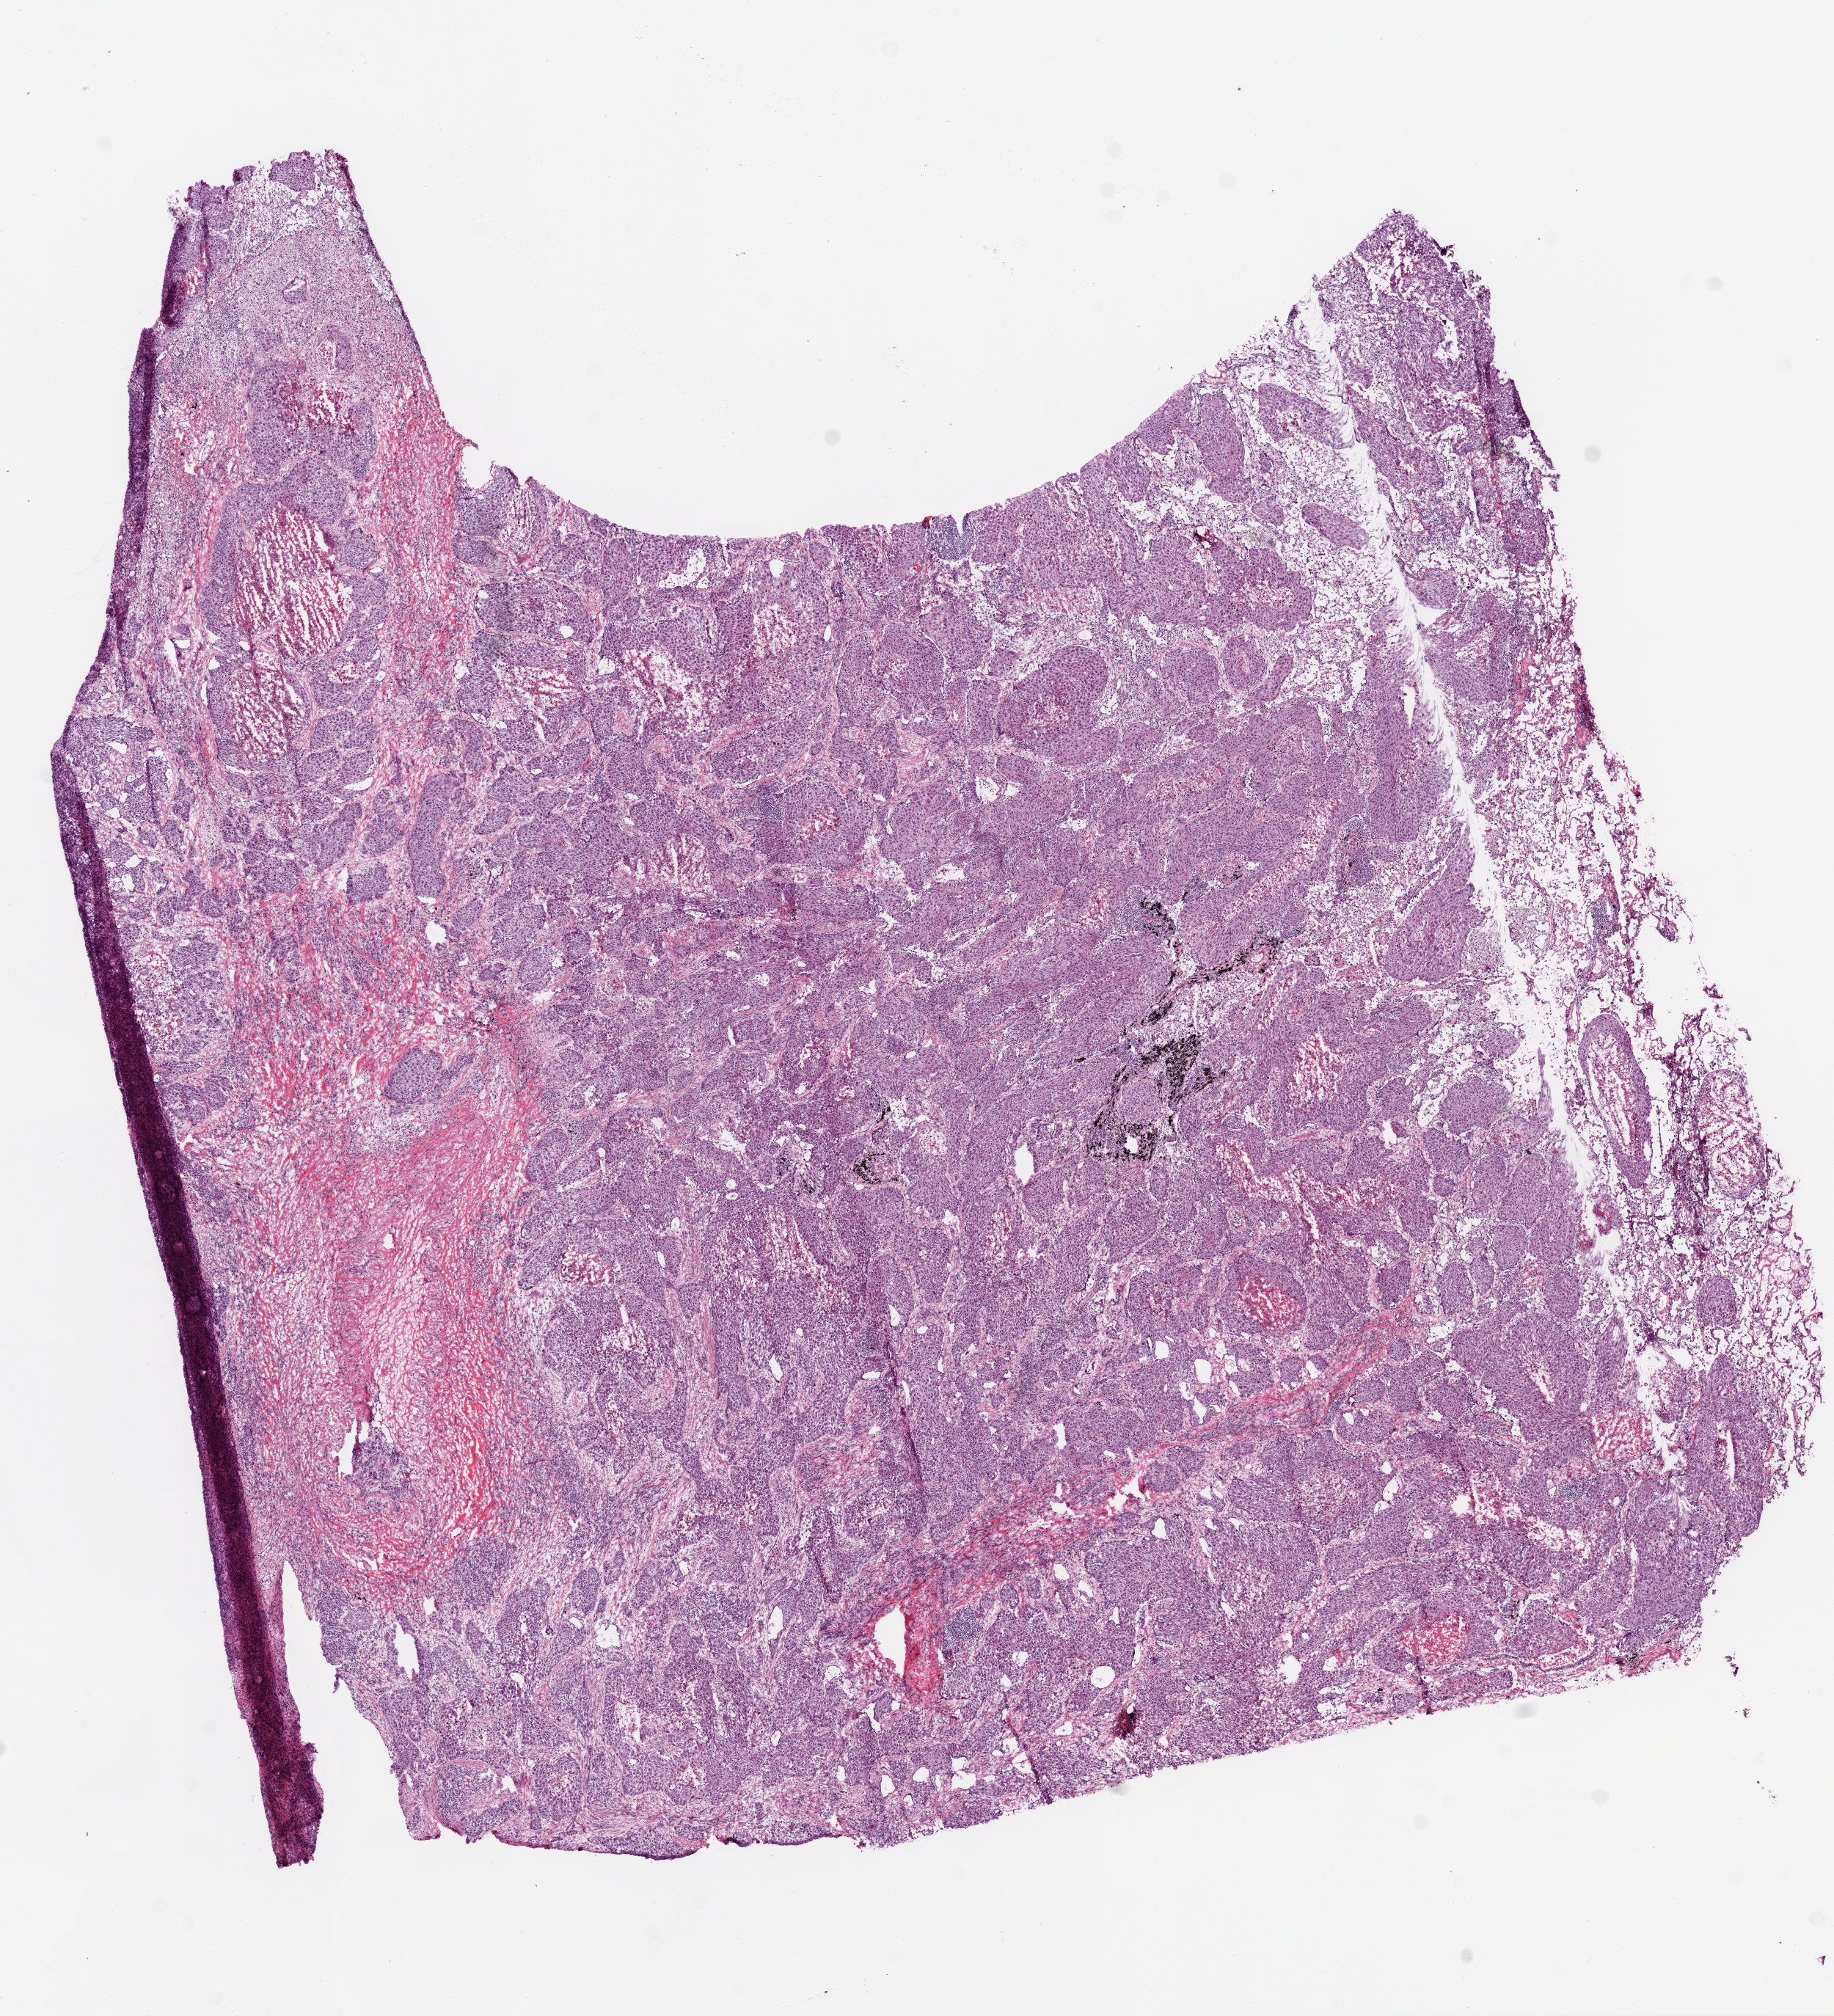
Digitized H&E-stained tissue section (whole slide) — shown as a low-resolution overview of the whole scanned area (about 10.0 x 11.0 mm, slide scanned at 20x), frozen section from the bottom of the tissue portion, primary tumour sample from the lung. Female, age 55 years at initial diagnosis. Slide review estimates, as recorded: tumour cells 80%, tumour nuclei 90%.
Pathologic diagnosis: Squamous cell carcinoma, NOS (lower lobe, lung).